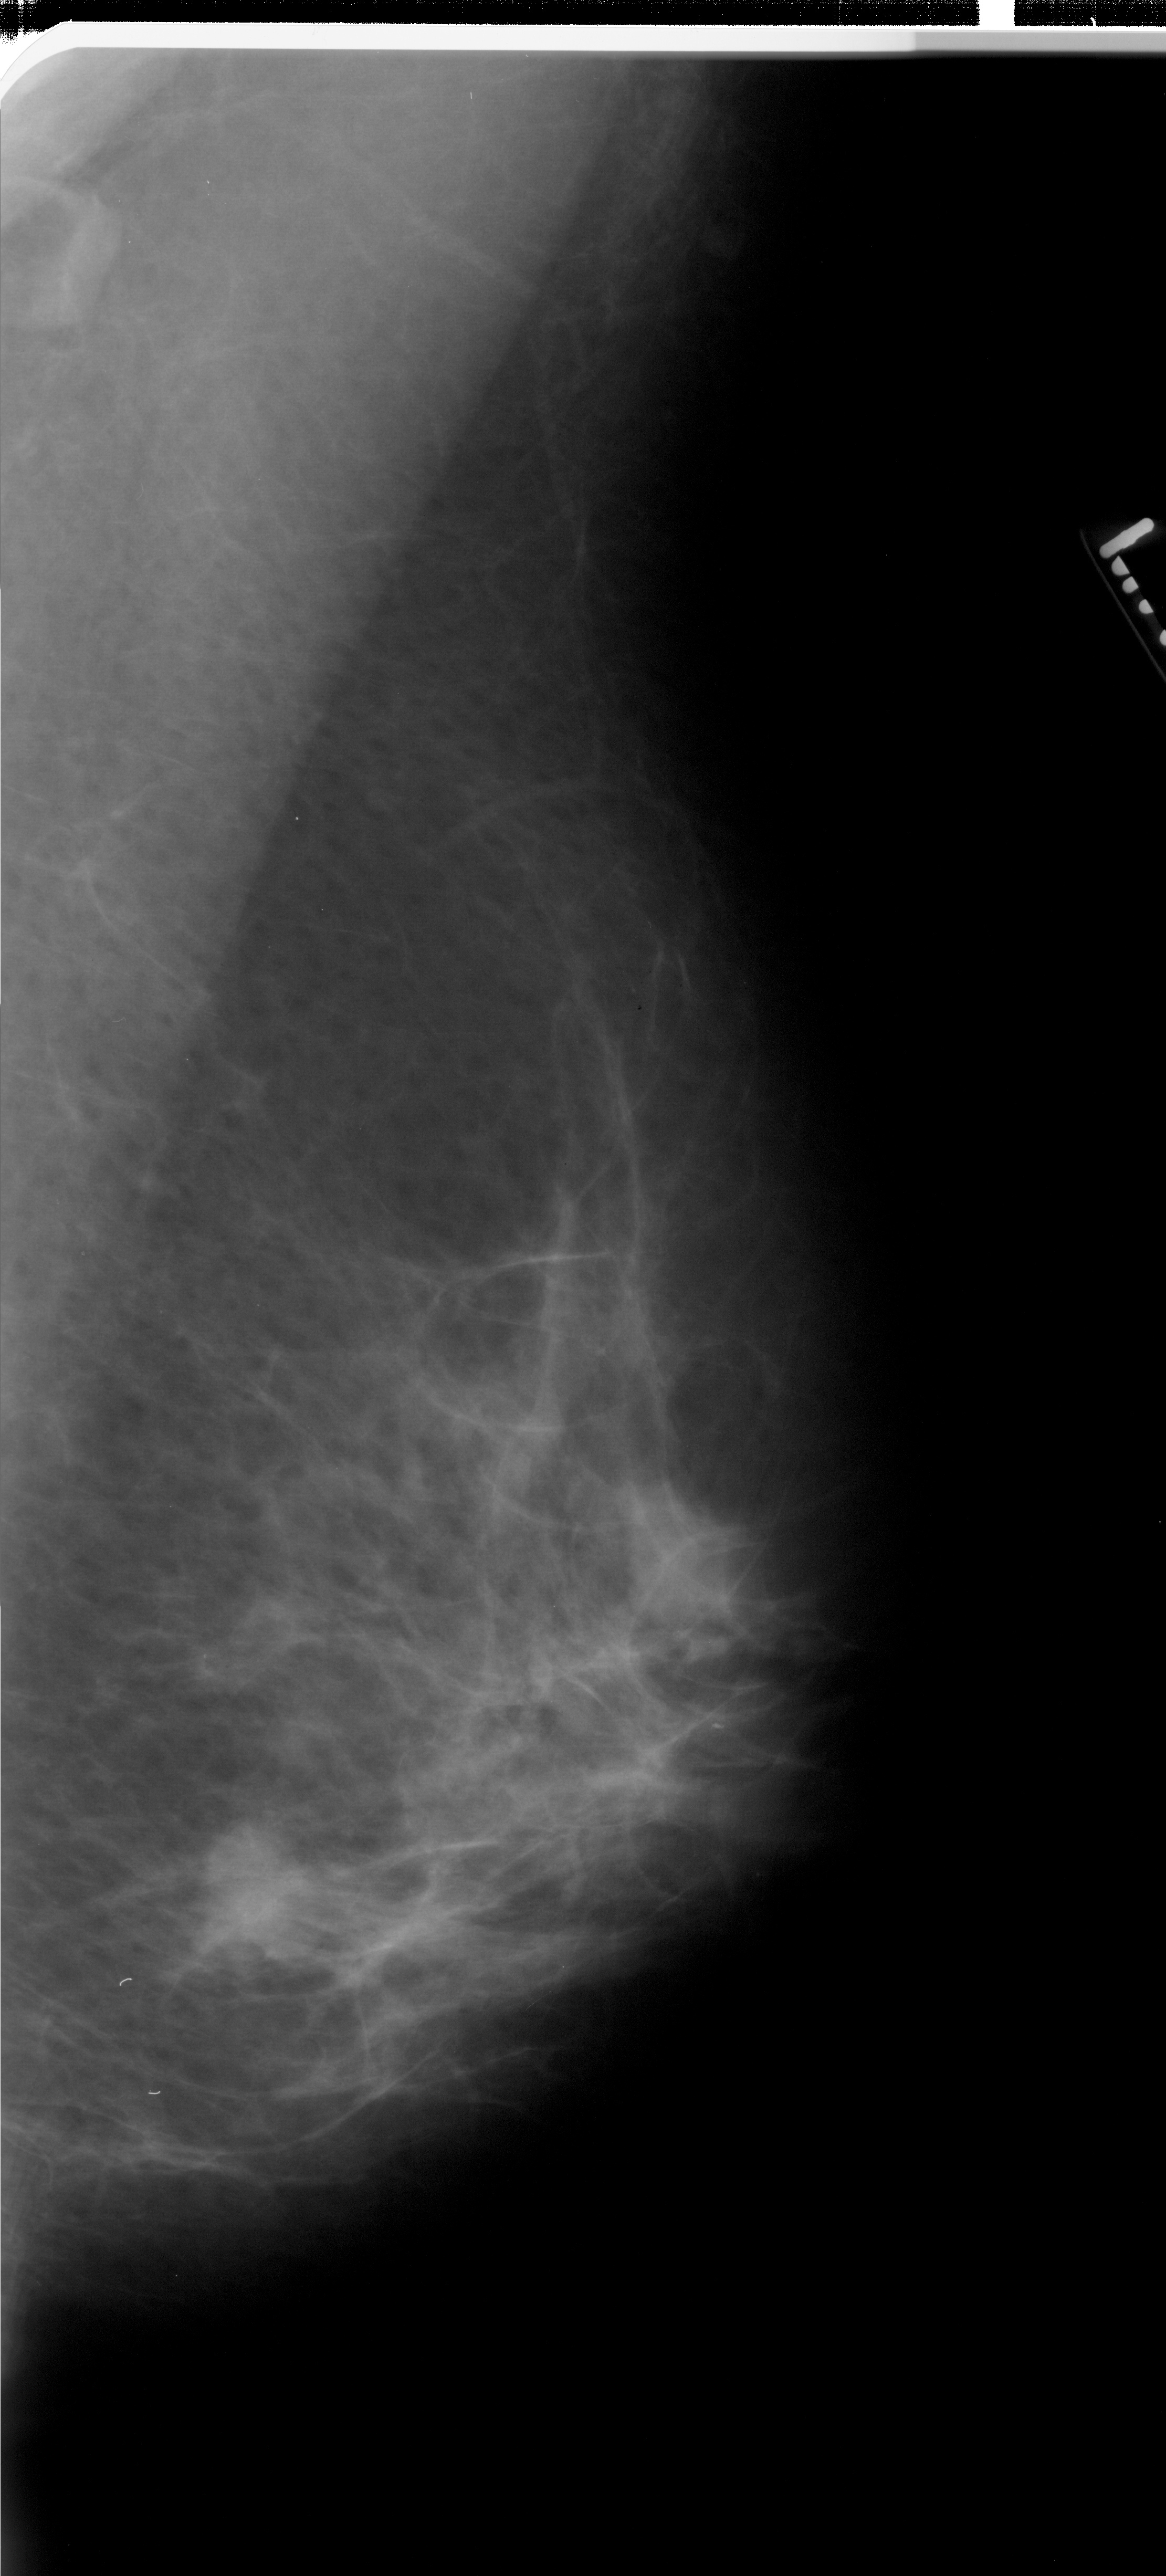
Mammogram (digitized film); right breast; mediolateral oblique (MLO) view; 1166 × 2576 image matrix.
Expert-marked regions of interest on this film, with their recorded descriptors:
- mass, shape lobulated, margins ill defined; BI-RADS assessment category 4; subtlety rating 4 on a 1 (subtle) to 5 (obvious) scale; pathology (as recorded): malignant: box from (x=195, y=1830) to (x=317, y=1957) px